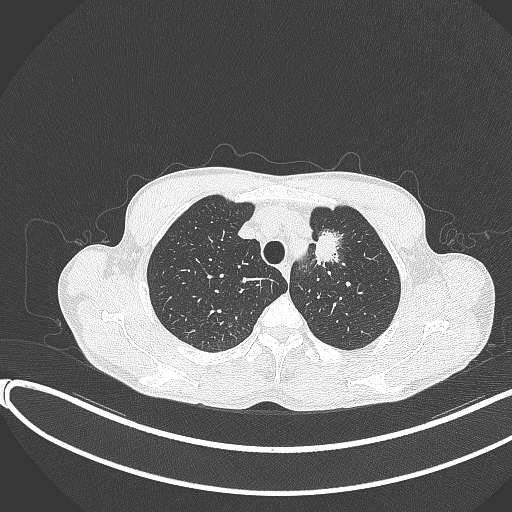
Chest CT, one axial slice; slice 313 of 374 in the series (ordered by position); reconstruction kernel B70f; 120 kVp; lung window (W 1500 / L -600 HU); 1 mm slice thickness; 512 × 512 image matrix, field of view 400 × 400 mm. Male patient, age 58 years. From the clinical record (not read from this slice): clinical TNM (as recorded): T1c N1 M0.
Structures marked on this image (rectangle marked by the reading radiologist):
- lung tumour (recorded histology: adenocarcinoma): bounding box (x1, y1, x2, y2) in pixels: (308, 224, 357, 281)